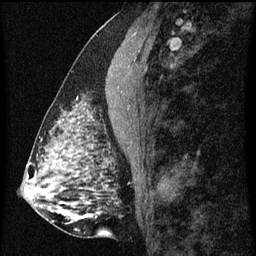
Breast MRI (dynamic contrast-enhanced), one sagittal slice; slice 26 of 60 in the series (ordered by position); dynamic contrast-enhanced series, image 2 of 3 at this slice position (ordered by acquisition); 1.5 T; TE 4.2 ms, TR 8 ms; 2 mm slice thickness; 256 × 256 image matrix, field of view 180 × 180 mm. Female patient, age 51 years.
Structures marked on this image (semi-automatic segmentation, software-assisted and operator-edited):
- analysis volume of interest (the breast-tissue region the enhancement analysis was run in; not a lesion): bounding box [x1, y1, x2, y2] px = [61, 86, 96, 129]
- tumour enhancement mask (voxels above the 70 % enhancement threshold inside the analysis volume of interest): [76, 106, 79, 115]